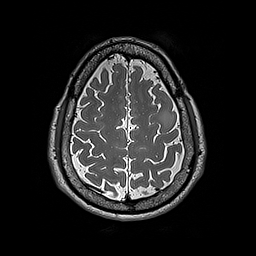
Brain MRI from a brain-tumour surgery series, one axial slice. Position 61 of 192 along the scan axis. 1 mm slice thickness. 256 × 256 image matrix, field of view 250 × 250 mm. From the clinical record (not read from this slice): histopathology: Astrocytoma; WHO grade: 2; IDH mutation: yes; tumour location: Left Frontal.
Outlined on this slice (outlined manually by an expert reader):
- tumour: box from (x=158, y=104) to (x=174, y=128) px